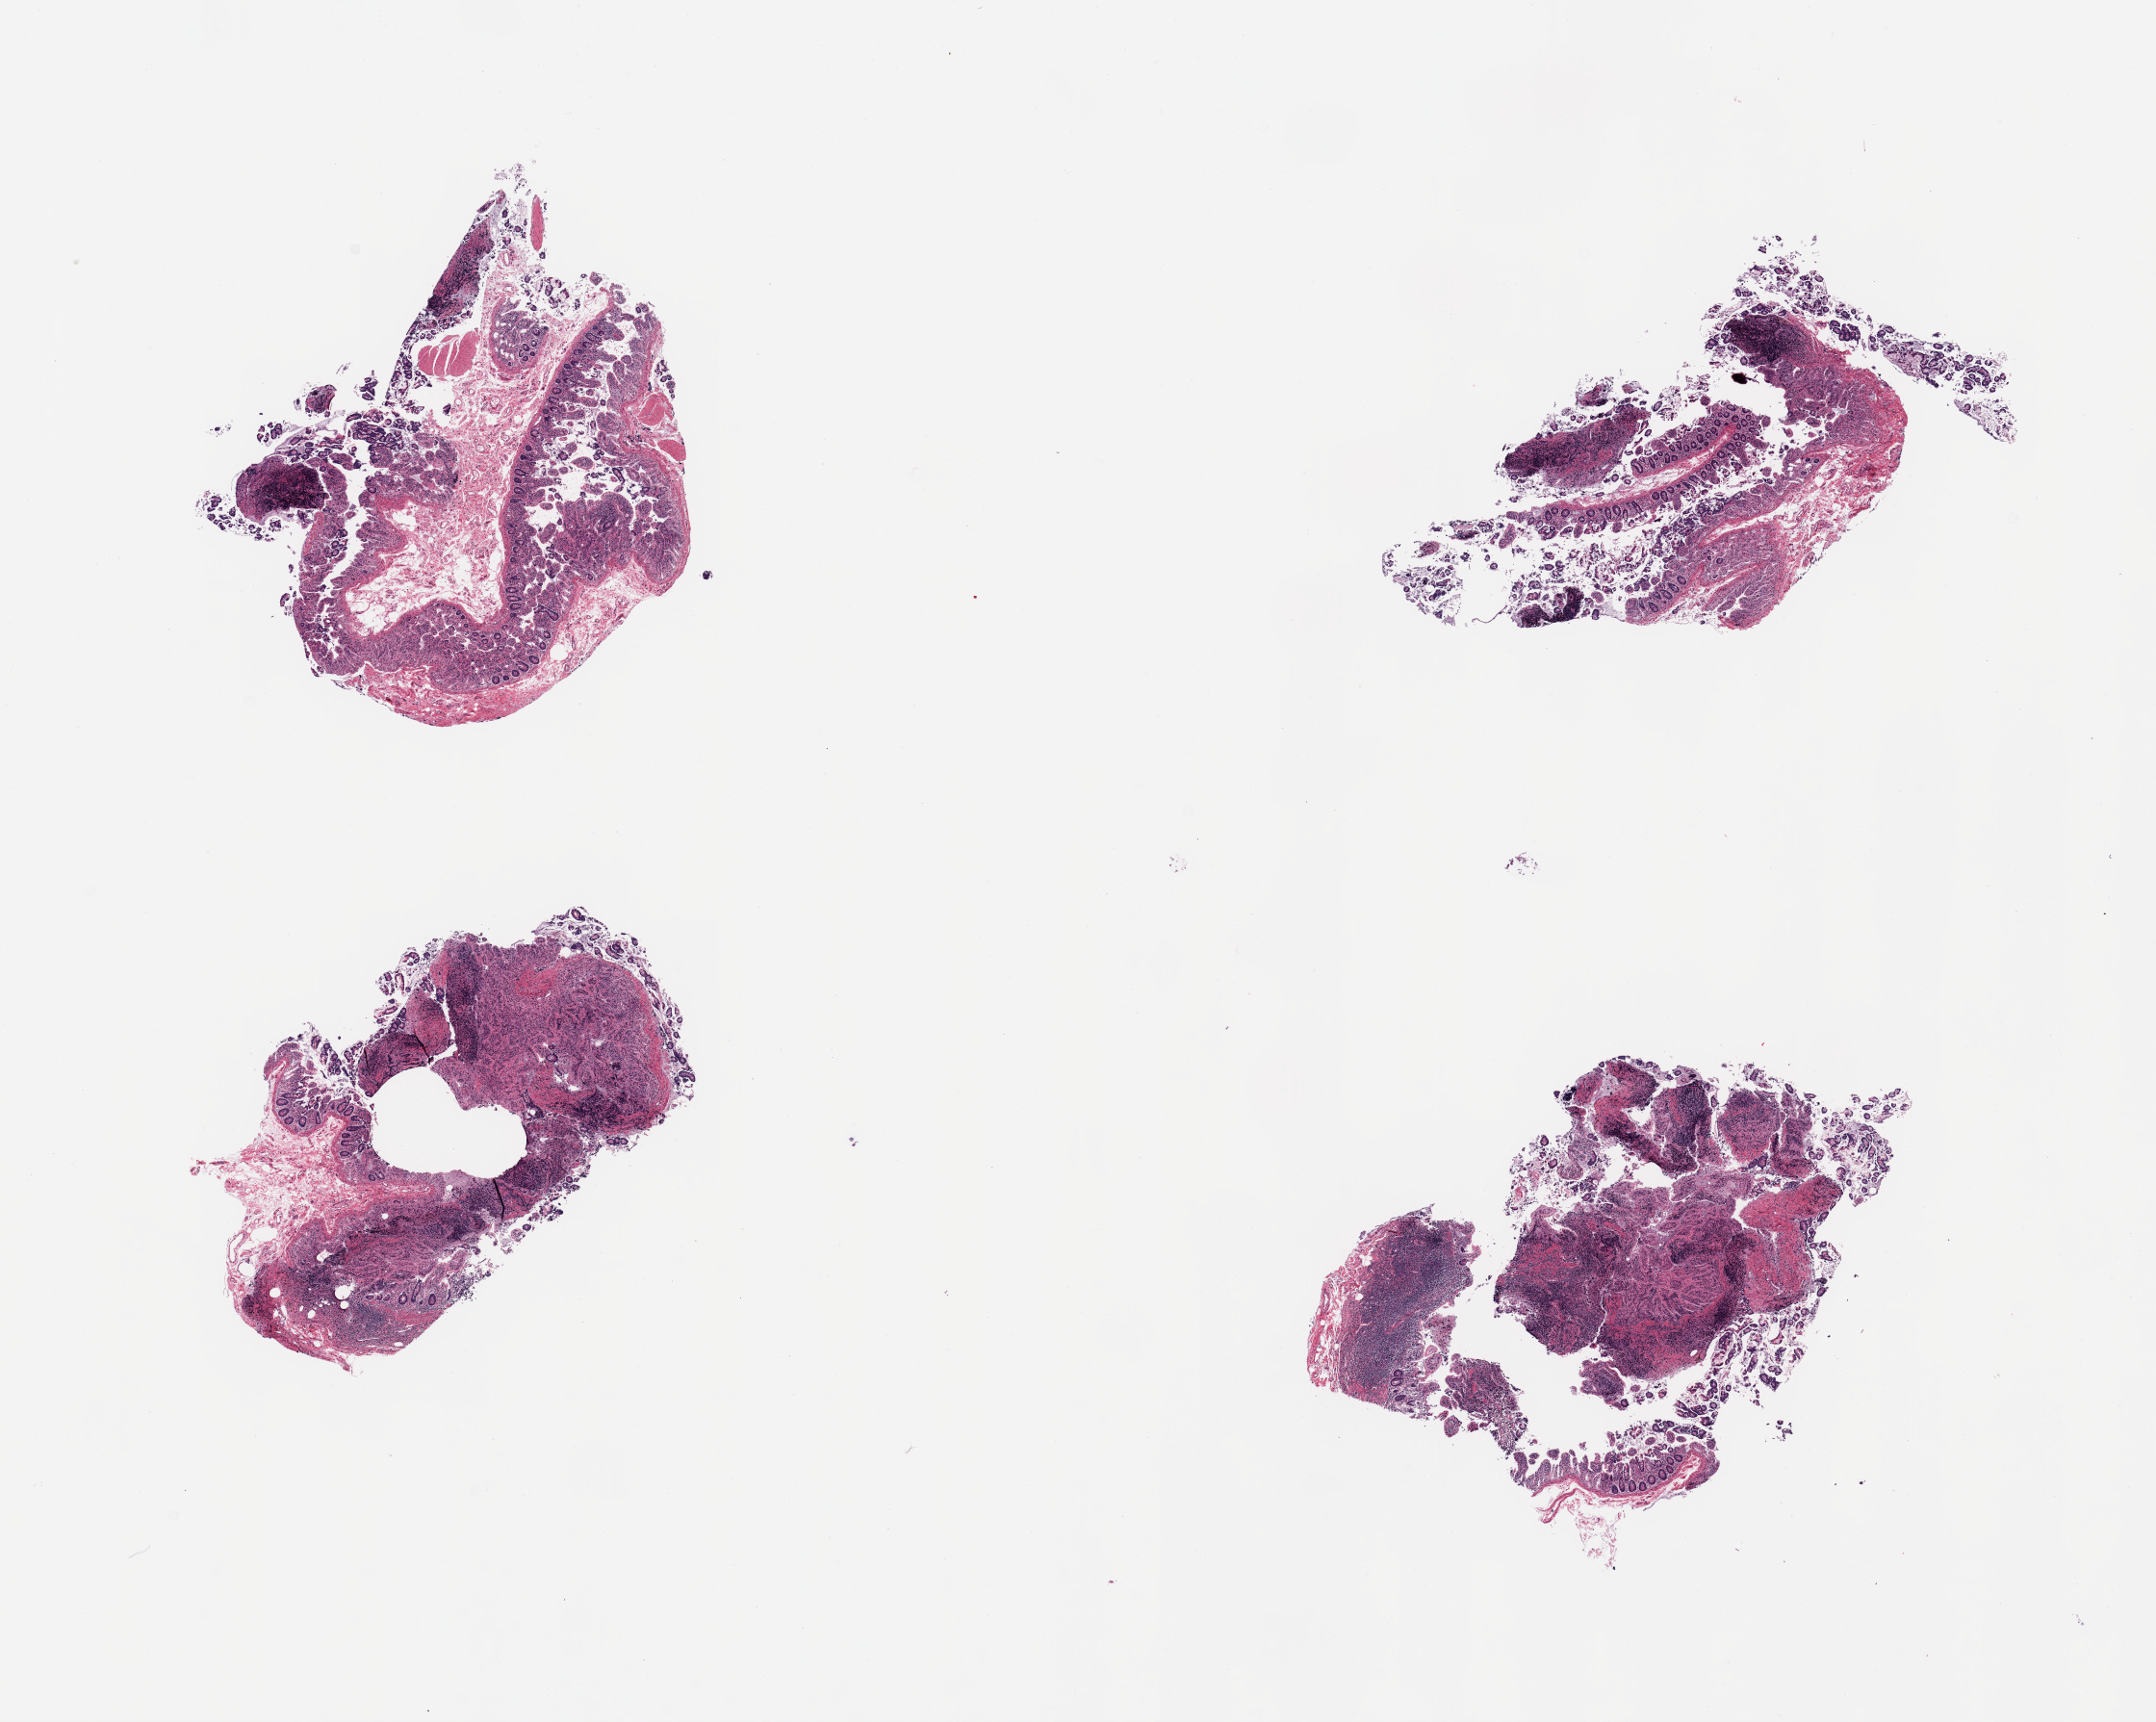
Digitized hematoxylin and eosin (H&E)-stained section, brightfield, whole scanned area (about 17.7 x 14.2 mm, acquisition: 20x scan) shown as a low-resolution overview; PAXgene-fixed paraffin-embedded (PFPE) section; sampled site (target tissue): ileum; donor tissue sample.
* review note (as recorded): 4 pieces, lymphoid aggregates are ~30% total tissue